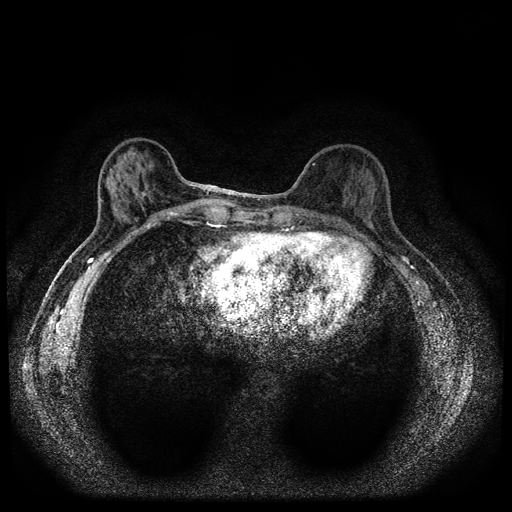
Breast MRI (dynamic contrast-enhanced, multi-phase), one axial slice. Slice 35 of 112 in the series (ordered by position). Dynamic contrast-enhanced series, time point 2 of 5 at this slice position (early post-contrast). 1.5 T. TE 2.7 ms, TR 5.4 ms. 2 mm slice thickness. 512 × 512 image matrix, field of view 320 × 320 mm. Patient: female, 61 years.
Annotated regions visible in this slice (semi-automatically segmented with operator editing):
- breast lesion (labelled benign in the annotation): bounding box <133,188,152,201> (left, top, right, bottom; pixels)